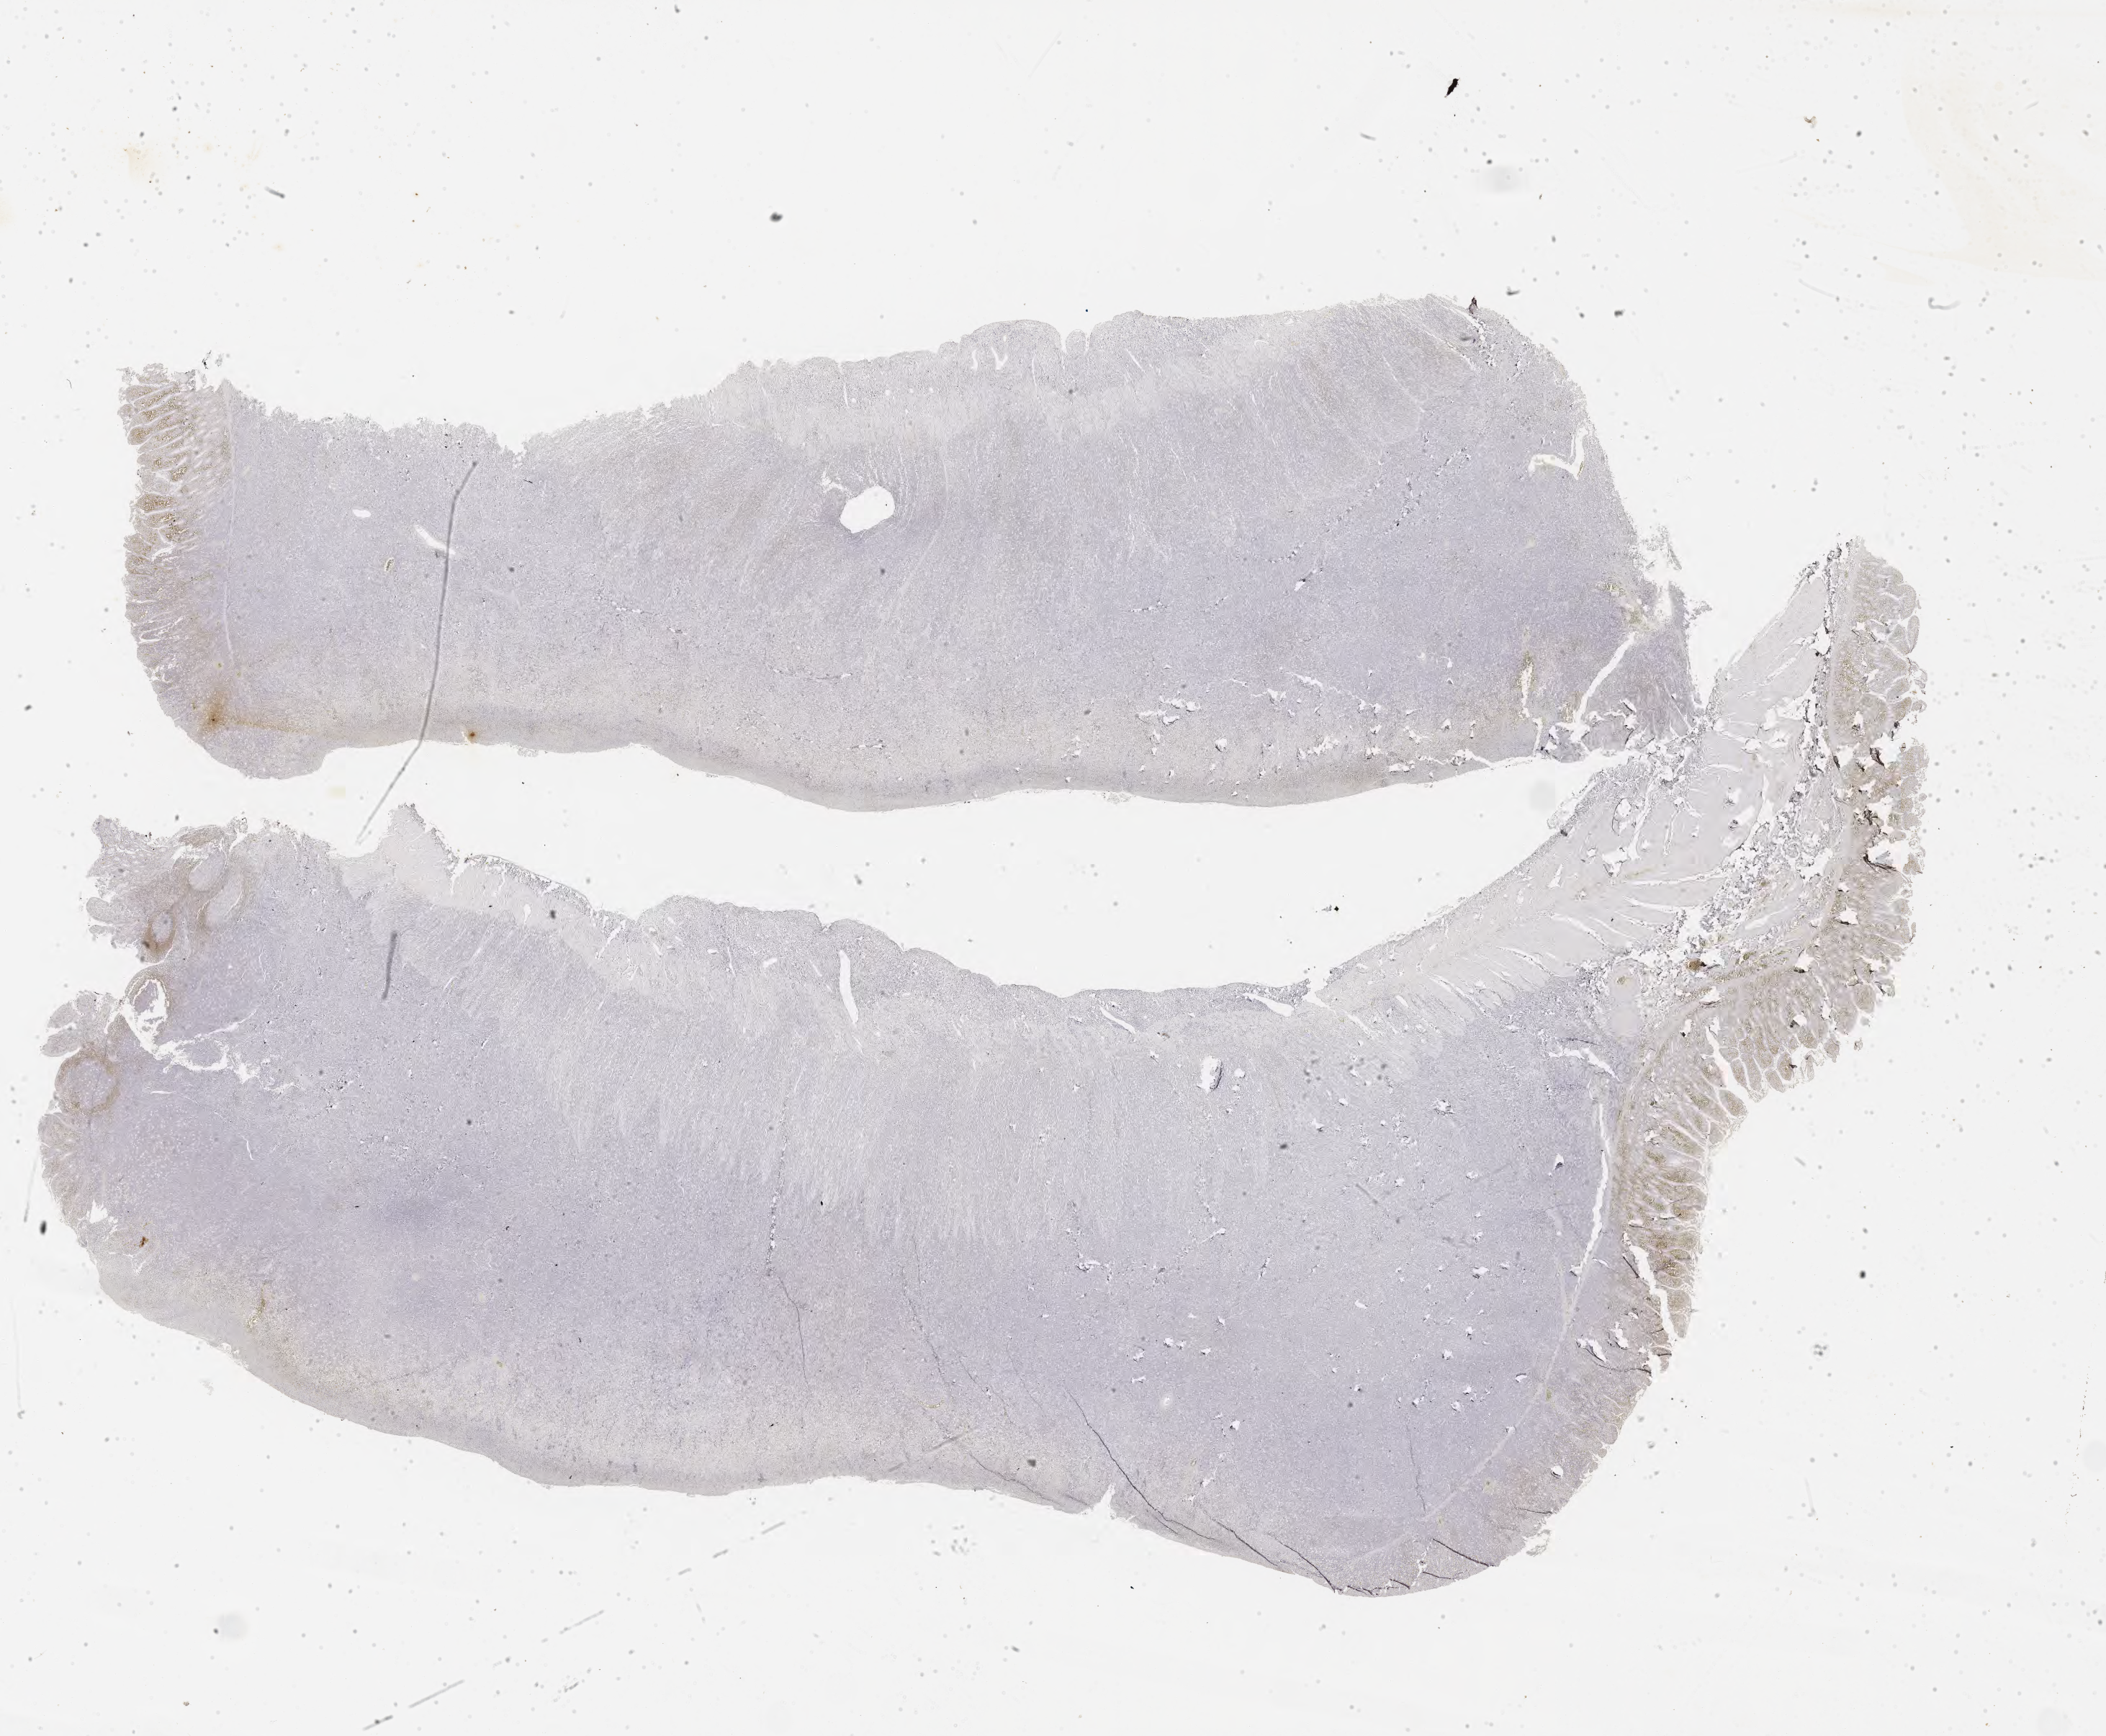
IHC for BCL2, whole-slide image, whole scanned area (about 23.6 x 19.5 mm) shown as a low-resolution overview; tumor tissue. Female patient, 27 years old.
• histologic diagnosis: Burkitt lymphoma, NOS